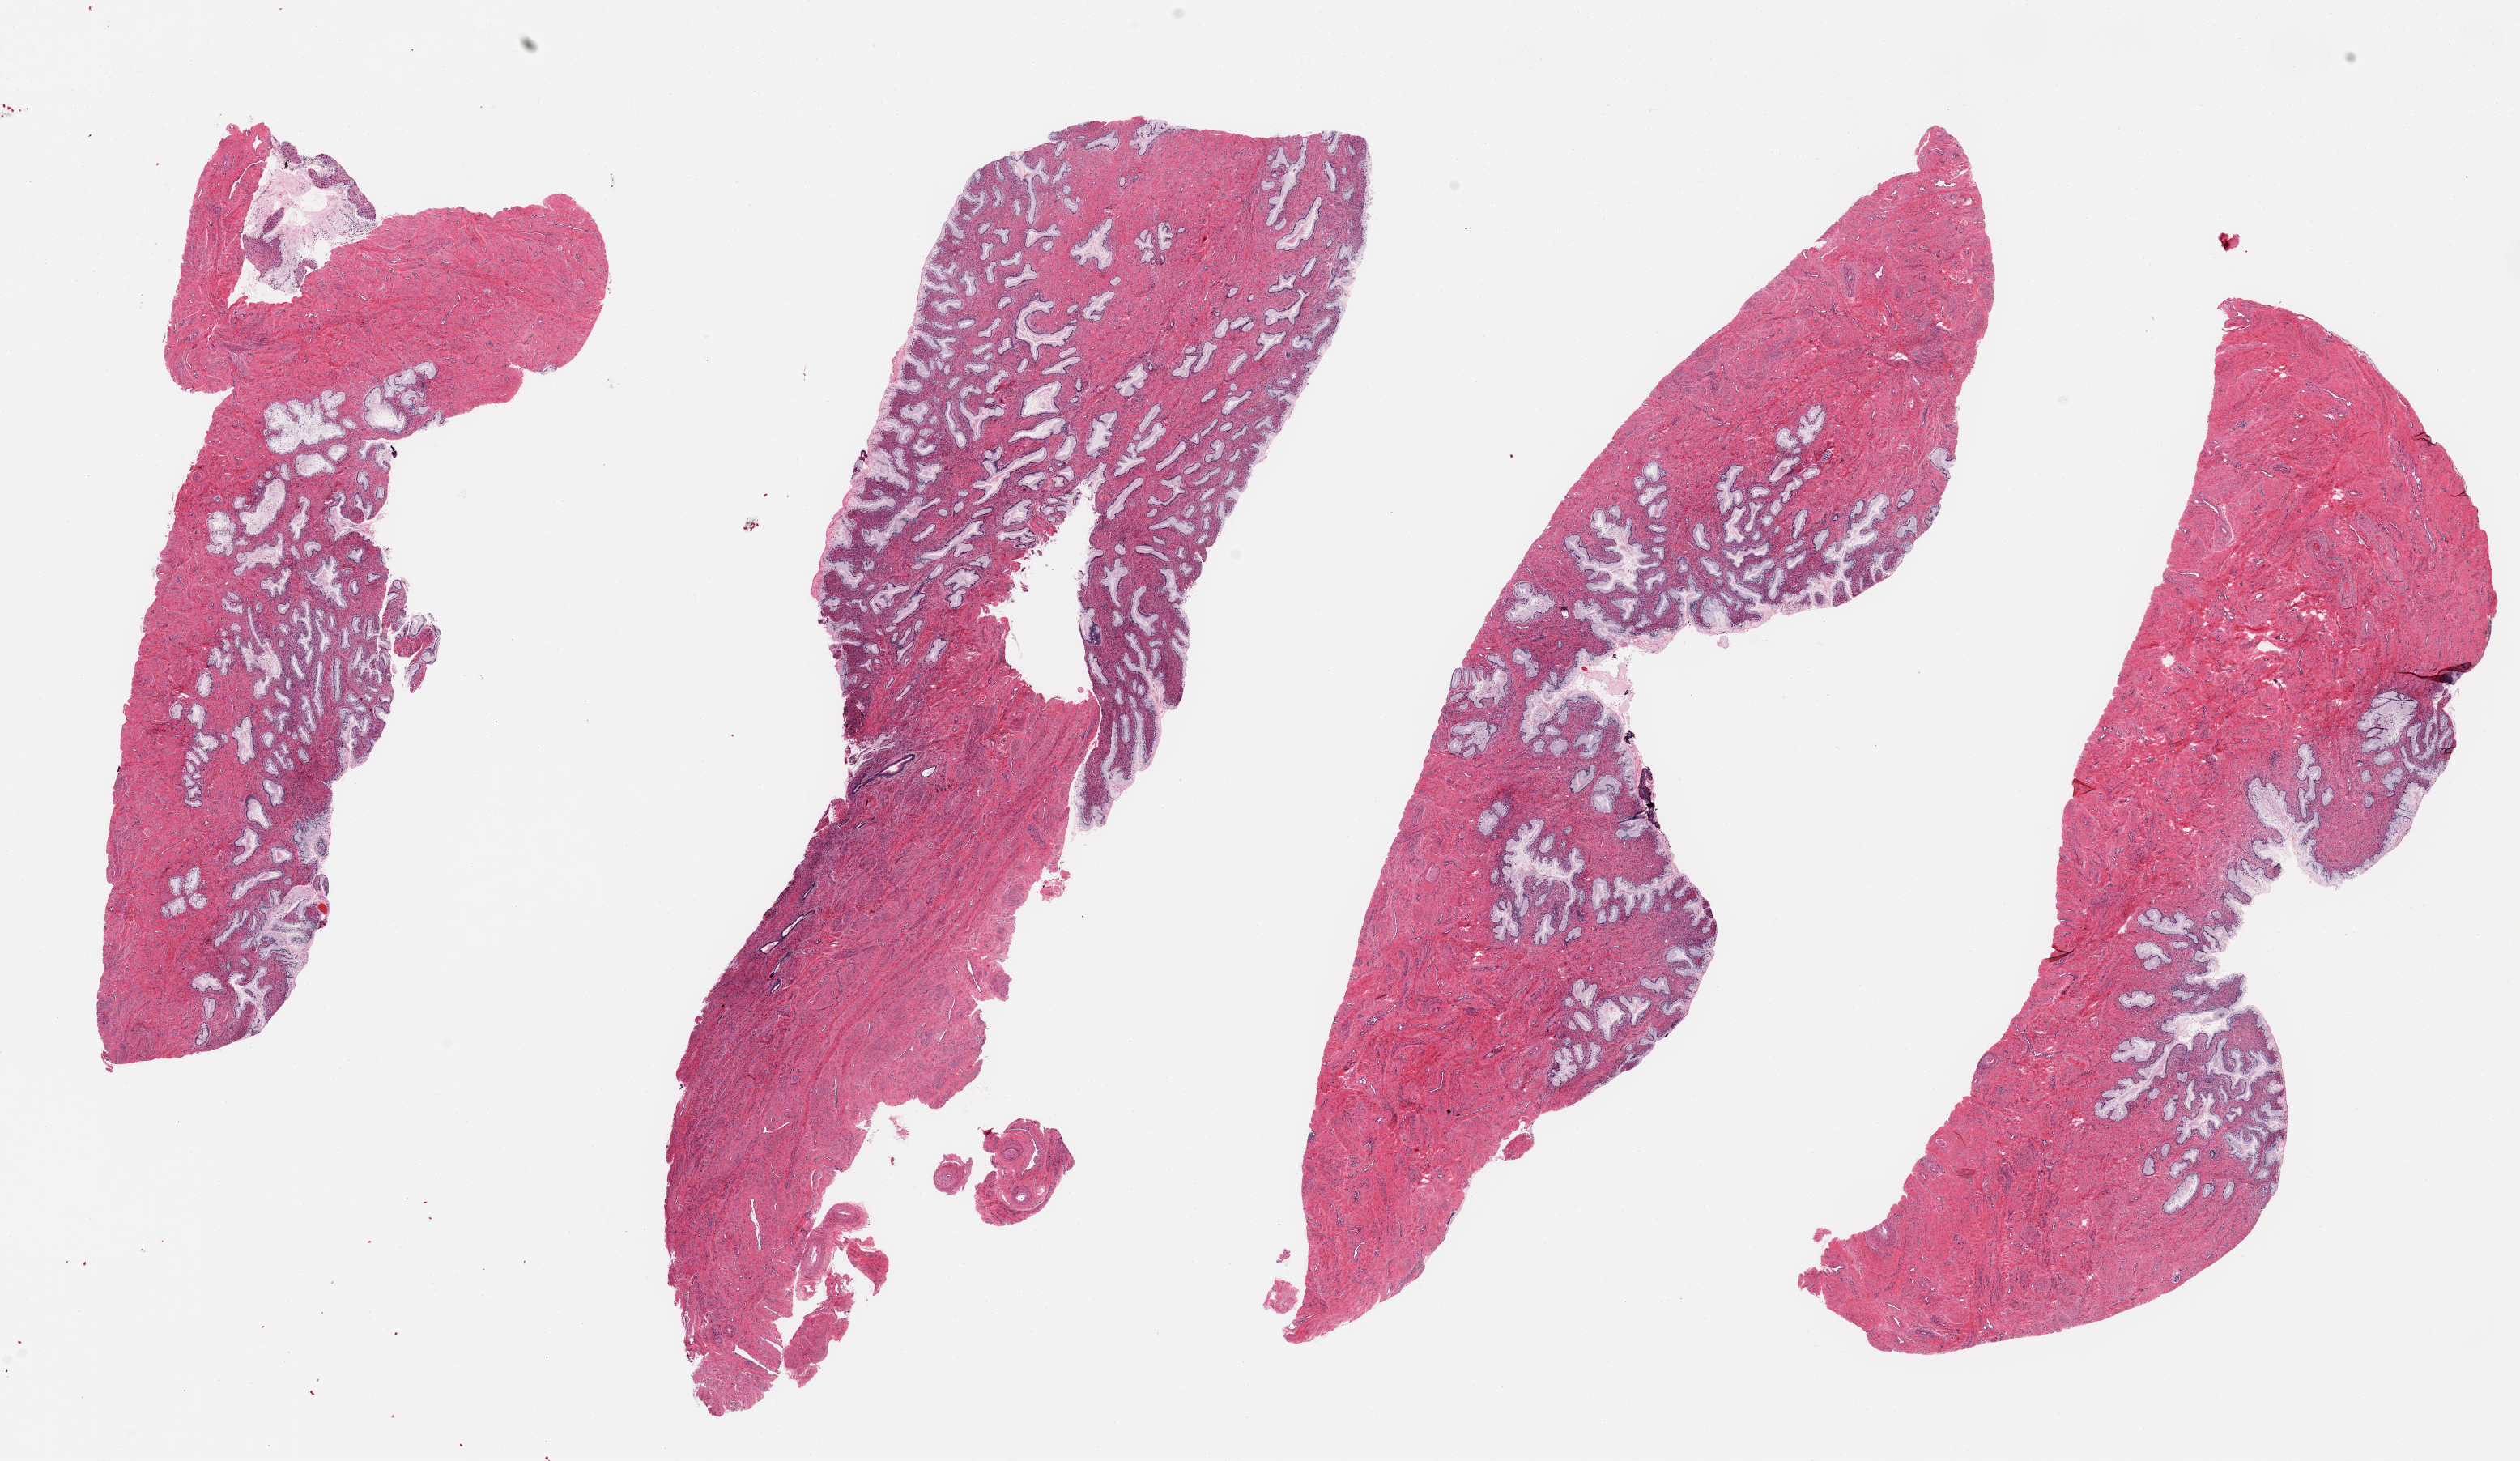
Digitized H&E-stained section — shown as a low-resolution overview of the whole scanned area (about 24.6 x 14.3 mm). PAXgene-fixed, paraffin-embedded tissue. Sampled site (target tissue): endocervix. Donor tissue sample. Donor sex: female.
Pathologist's review note for this sample: 4 pieces, up to 14x4 mm; ECTOCERVIX not endo.